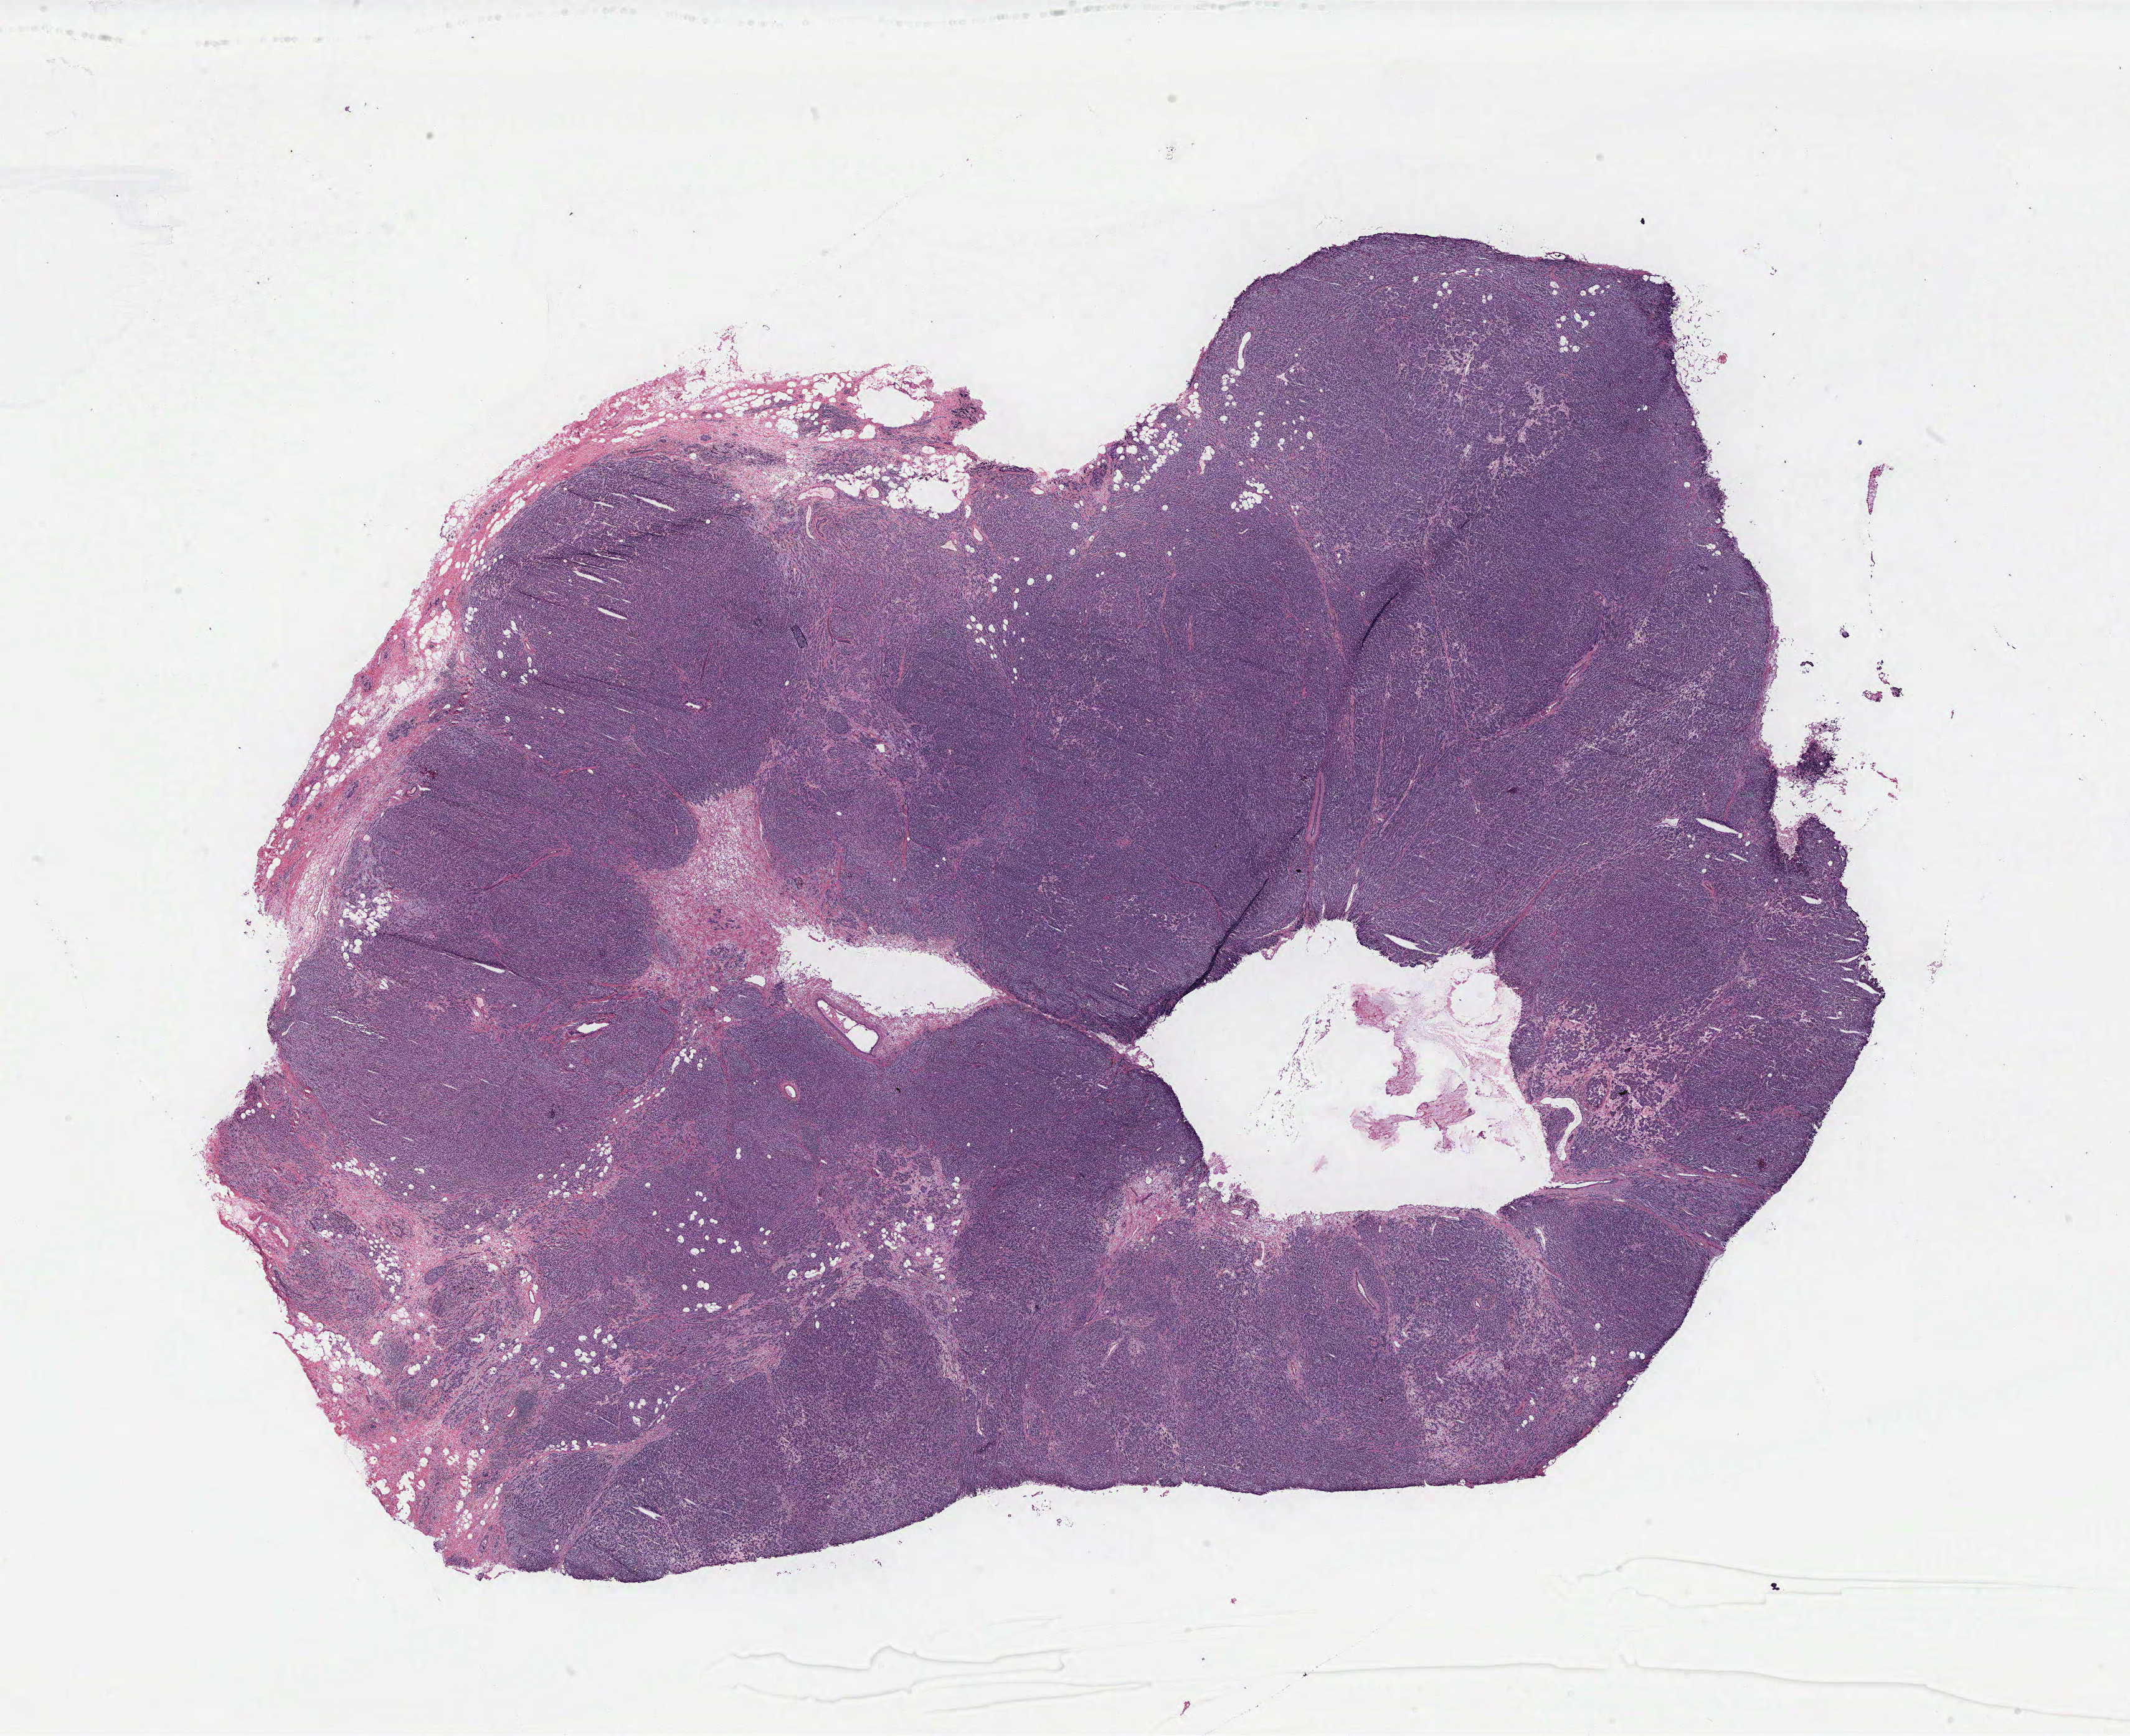
Digitized H&E-stained tissue section (whole slide), a low-resolution overview of the entire scanned area, about 27.4 x 22.3 mm (slide scanned at 40x); breast, tissue type not recorded. Female, 43 y/o.
Patient diagnosis: Infiltrating duct carcinoma, NOS.